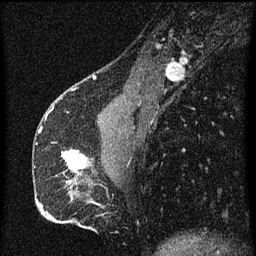
Breast MRI (dynamic contrast-enhanced), one sagittal slice; position 23 of 60 along the scan axis; dynamic contrast-enhanced series, image 2 of 3 at this slice position (ordered by acquisition); 1.5 T; TE 4.2 ms, TR 8 ms; 256 × 256 image matrix, field of view 180 × 180 mm. Female patient, age 51 years.
Structures marked on this image (semi-automatically segmented with operator editing):
- analysis volume of interest (the breast-tissue region the enhancement analysis was run in; not a lesion): bounding box (x1, y1, x2, y2) in pixels: (62, 150, 93, 175)
- tumour enhancement mask (voxels above the 70 % enhancement threshold inside the analysis volume of interest): (62, 150, 87, 173)